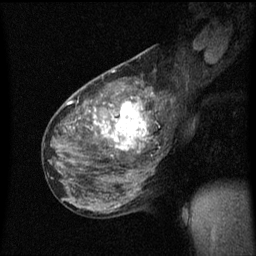
Breast MRI (dynamic contrast-enhanced), one sagittal slice. Position 30 of 60 along the scan axis. Dynamic contrast-enhanced series, image 2 of 3 at this slice position (ordered by acquisition). 1.5 T. TE 4.2 ms, TR 8.4 ms. 256 × 256 image matrix. Patient: female, 49 years.
Annotated regions visible in this slice (semi-automatic segmentation, software-assisted and operator-edited):
- analysis volume of interest (the breast-tissue region the enhancement analysis was run in; not a lesion): bounding box <103,90,157,151> (left, top, right, bottom; pixels)
- tumour enhancement mask (voxels above the 70 % enhancement threshold inside the analysis volume of interest): <103,94,153,151>